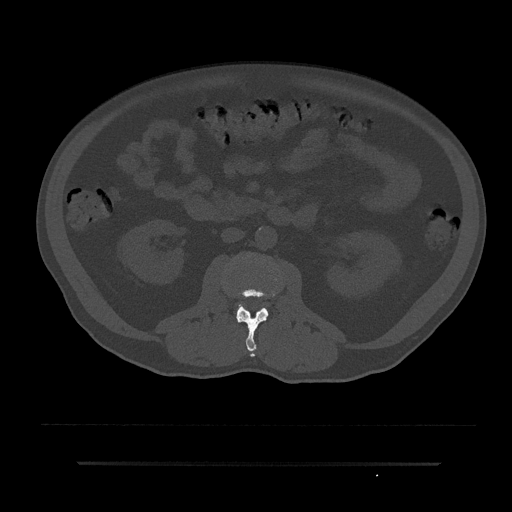
CT including the spine, one axial slice; position 49 of 797 along the scan axis; reconstruction kernel Br40s/3; 120 kVp; bone window (W 1800 / L 400 HU); 0.5 mm slice thickness; 512 × 512 image matrix, field of view 464 × 464 mm. Male patient, age 59 years. Case-level facts recorded for this patient, not image findings: primary cancer: bile ducts.
Outlined on this slice (semi-automatically segmented with operator editing):
- L2 vertebra: bounding box (x1, y1, x2, y2) in pixels: (232, 265, 279, 357)